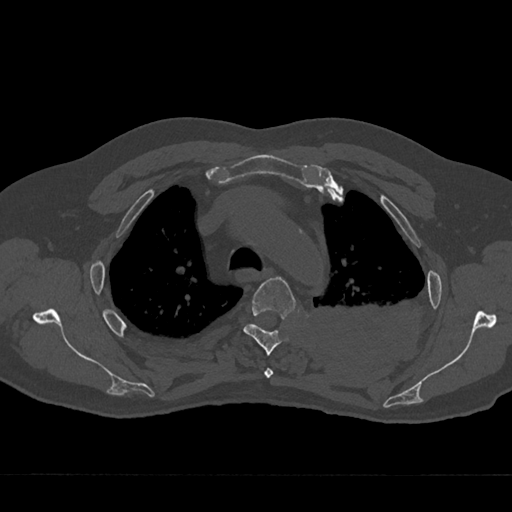
CT including the spine, one axial slice; slice 523 of 797 in the series (ordered by position); reconstruction kernel Br40s/3; bone window (W 1800 / L 400 HU); 0.5 mm slice thickness; 512 × 512 image matrix. Male patient, age 75 years. From the clinical record (not read from this slice): primary cancer: renal; vertebrae with lytic lesions (as recorded): T4.
Annotated regions visible in this slice (semi-automatic segmentation, software-assisted and operator-edited):
- T3 vertebra: bounding box [x1, y1, x2, y2] px = [264, 368, 273, 378]
- T4 vertebra: [243, 276, 296, 356]